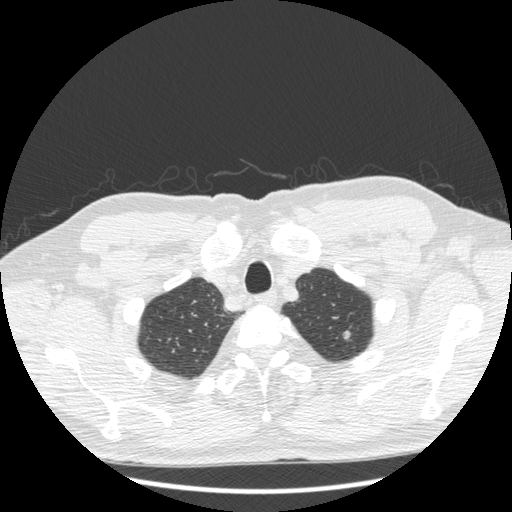
Low-dose screening chest CT, one axial slice. Reconstruction kernel STANDARD. 120 kVp. Lung window (W 1500 / L -600 HU). 512 × 512 image matrix, field of view 380 × 380 mm.
Outlined on this slice (expert manual segmentation):
- lesion 1 (tumor, upper lobe of left lung): box from (x=344, y=331) to (x=350, y=339) px